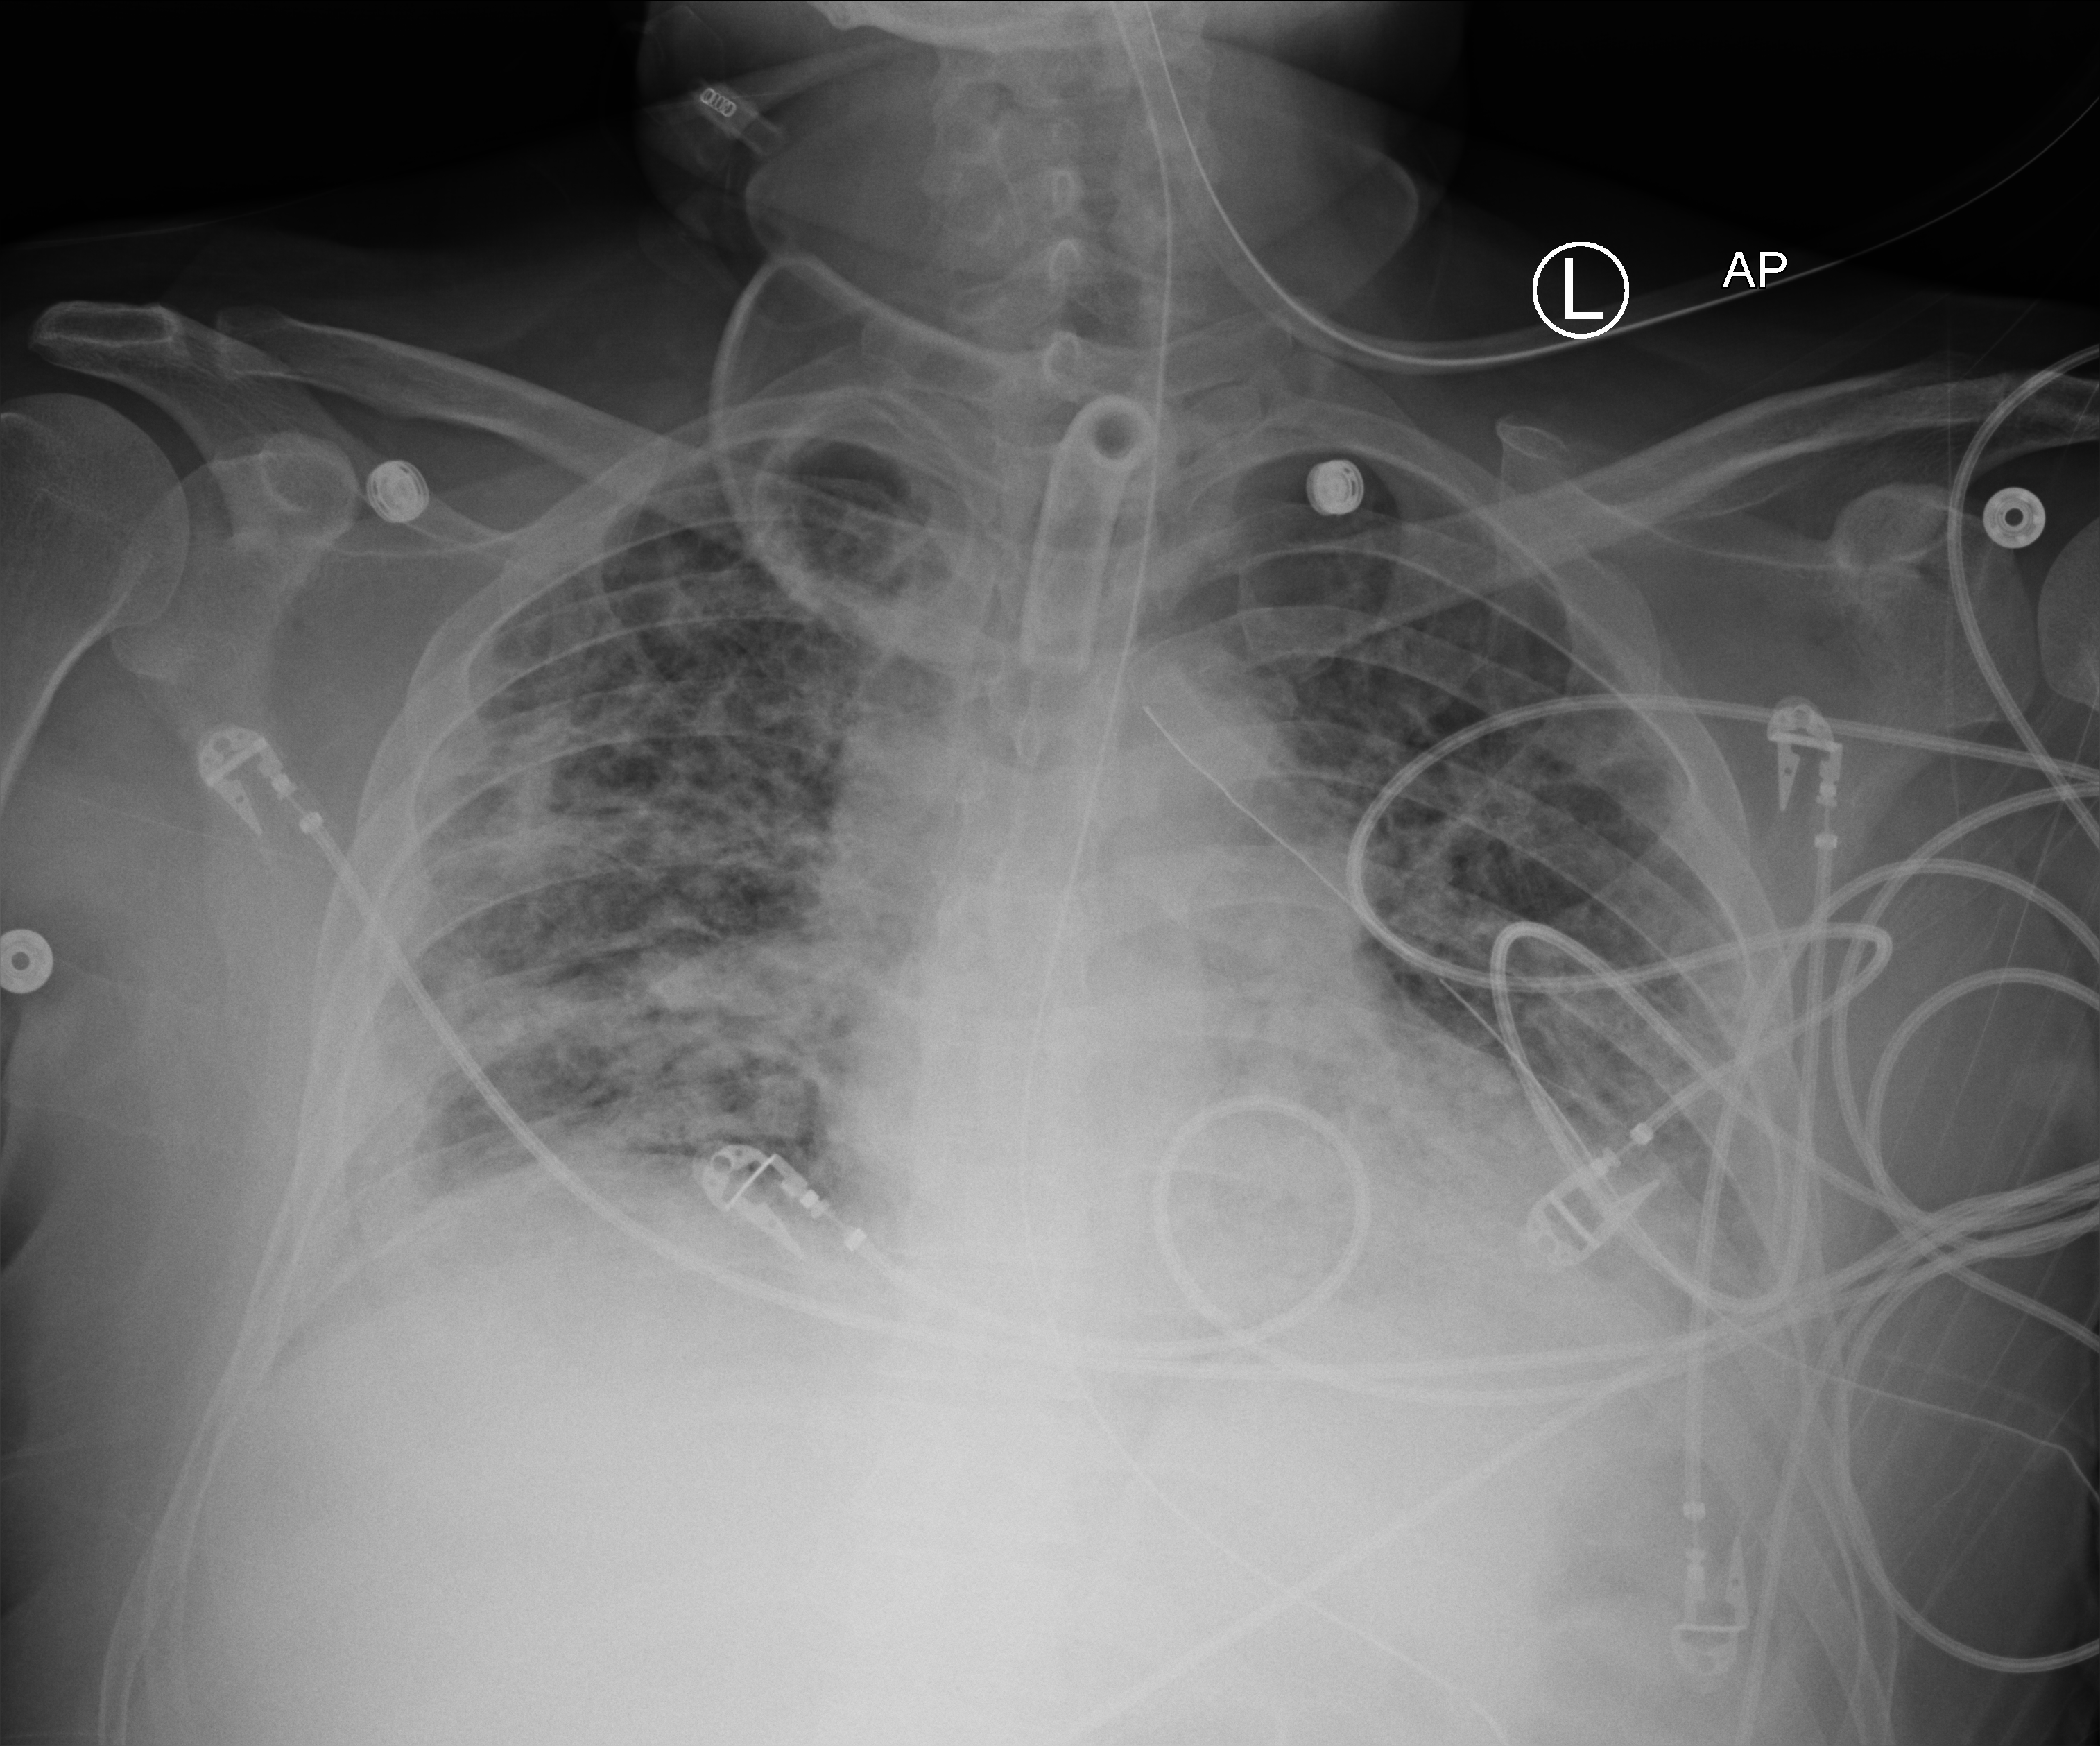
Bedside chest radiograph (computed radiography); anteroposterior (AP) projection. Male patient hospitalised with COVID-19, age 18–59 years.
From the hospital-stay record, not from the radiograph (when in the stay this image was taken is not recorded): mechanically ventilated during this hospital stay: yes; diabetes (admission record): yes; admitted to intensive care during this hospital stay: yes.